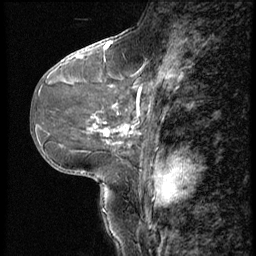
Breast MRI (dynamic contrast-enhanced), one sagittal slice. Position 26 of 56 along the scan axis. 3 images stored at this slice position (order not interpretable as contrast timing). 1.5 T. TE 4.2 ms, TR 9 ms. 2.5 mm slice thickness. 256 × 256 image matrix, field of view 180 × 180 mm. Patient: female, 46 years. From the clinical record (not read from this slice): setting: breast cancer imaged before/during neoadjuvant chemotherapy; receptor status: HER2-positive.
Outlined on this slice (semi-automatically segmented with operator editing):
- analysis volume of interest (the breast-tissue region the enhancement analysis was run in; not a lesion): bounding box <79,68,190,143> (left, top, right, bottom; pixels)
- tumour enhancement mask (voxels above the 140 % enhancement threshold inside the analysis volume of interest): <104,100,140,135>